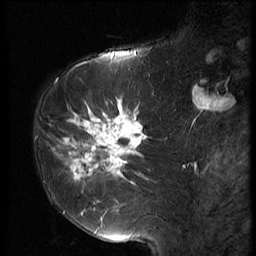
Breast MRI (dynamic contrast-enhanced), one sagittal slice. 3 images stored at this slice position (order not interpretable as contrast timing). 1.5 T. TE 4.2 ms, TR 9 ms. 256 × 256 image matrix. Patient: female, 61 years. Case-level facts recorded for this patient, not image findings: setting: breast cancer imaged before/during neoadjuvant chemotherapy; receptor status: HR-positive, HER2-negative.
Structures marked on this image (semi-automatically segmented with operator editing):
- analysis volume of interest (the breast-tissue region the enhancement analysis was run in; not a lesion): bounding box (x1, y1, x2, y2) in pixels: (47, 89, 153, 191)
- tumour enhancement mask (voxels above the 140 % enhancement threshold inside the analysis volume of interest): (51, 101, 147, 180)